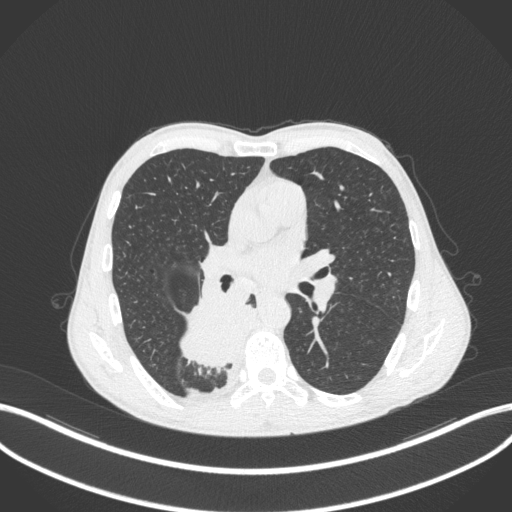
Chest CT, one axial slice. Position 205 of 371 along the scan axis. Reconstruction kernel B31f. Lung window (W 1500 / L -600 HU). 1 mm slice thickness. 512 × 512 image matrix, field of view 400 × 400 mm. Male patient, age 58 years. Case-level facts recorded for this patient, not image findings: clinical TNM (as recorded): T3 N1 M1.
Annotated regions visible in this slice (bounding box drawn by a radiologist):
- lung tumour (recorded histology: squamous cell carcinoma): bounding box [x1, y1, x2, y2] px = [176, 295, 257, 372]